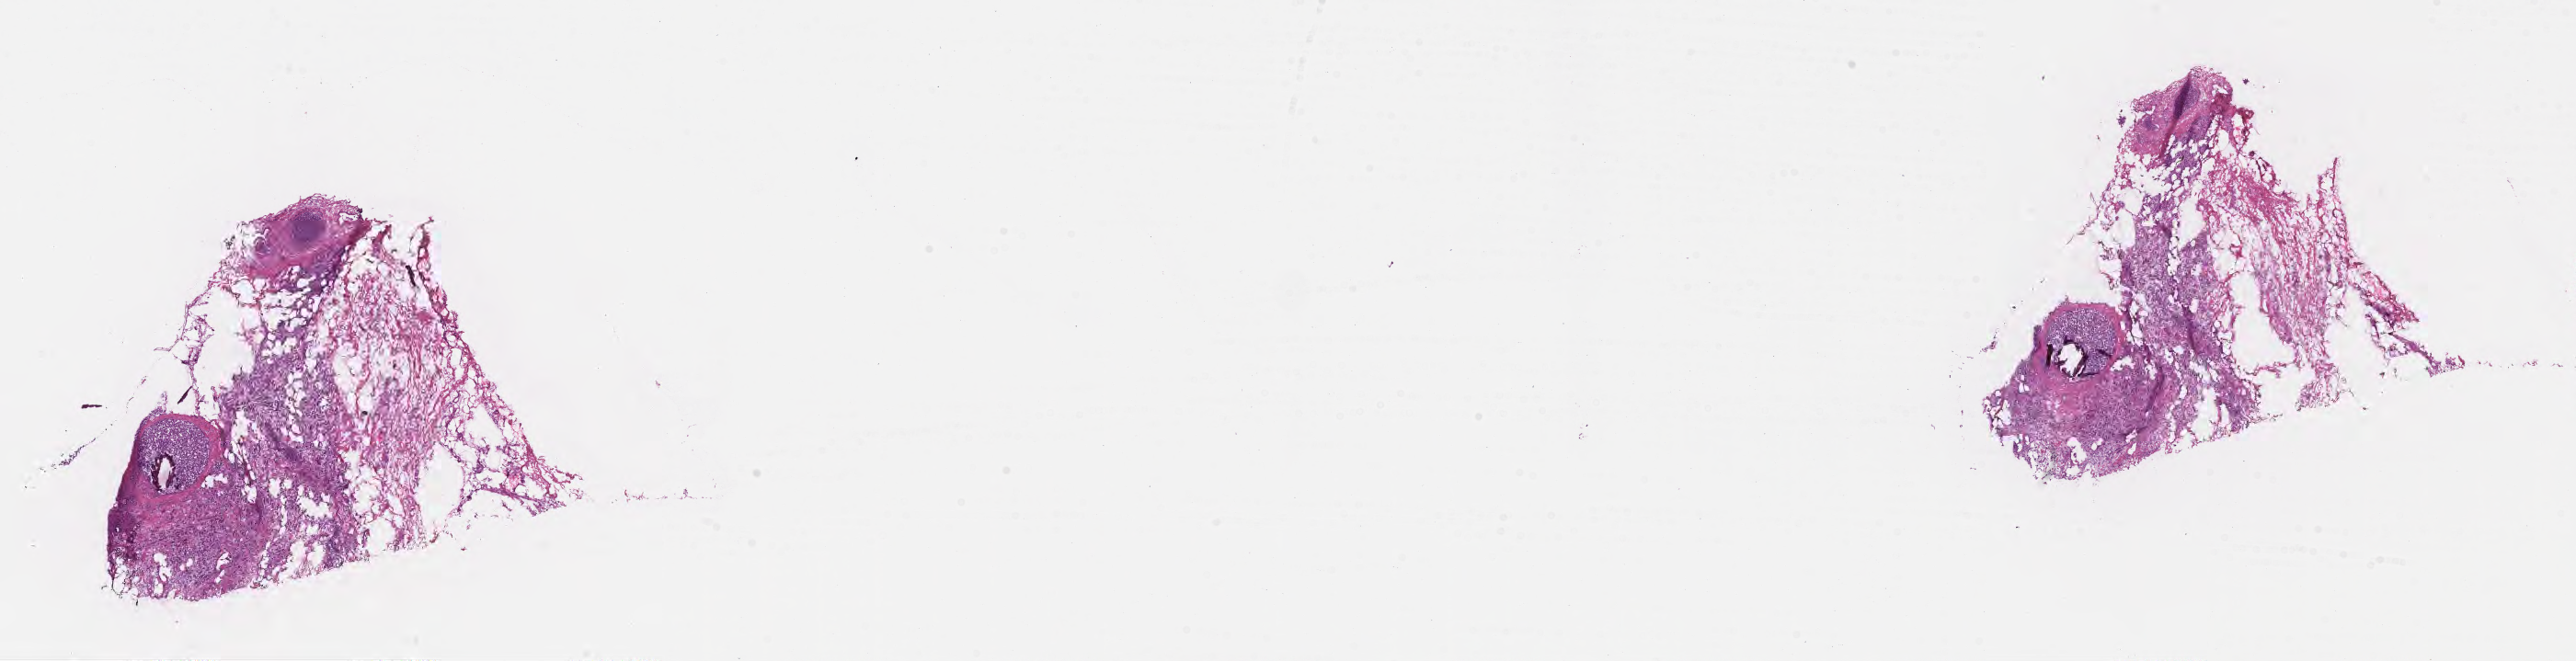
Haematoxylin and eosin whole-slide image, low-resolution overview of the scanned area, about 22.6 x 5.8 mm, frozen section, primary tumor, site: breast. Patient: female, age at initial diagnosis 60 years. Tumor grade: G3 (poorly differentiated). Slide review estimates, as recorded: tumor cells 62%, tumor nuclei 90%, stromal cells 38%, necrosis 0%, normal cells 0%. Infiltration values recorded for this section: lymphocyte infiltration 7%, monocyte infiltration 1%, neutrophil infiltration 0%.
Section: bottom of the tissue portion. Histologic diagnosis: Pleomorphic carcinoma. AJCC pathologic stage: Stage IA.